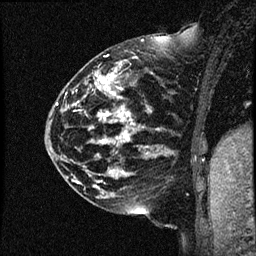
Breast MRI (dynamic contrast-enhanced), one sagittal slice; position 16 of 44 along the scan axis; dynamic contrast-enhanced study with each time point stored as its own series, time point 2 of 4 at this slice position (early post-contrast, ordered by acquisition time); 1.5 T; TE 4.2 ms, TR 17.7 ms; 2 mm slice thickness; 256 × 256 image matrix, field of view 200 × 200 mm. Female patient, age 52 years. From the clinical record (not read from this slice): setting: breast cancer imaged before/during neoadjuvant chemotherapy; receptor status: HR-positive, HER2-negative.
Outlined on this slice (semi-automatically segmented with operator editing):
- analysis volume of interest (the breast-tissue region the enhancement analysis was run in; not a lesion): bounding box (x1, y1, x2, y2) in pixels: (47, 48, 163, 147)
- tumour enhancement mask (voxels above the 100 % enhancement threshold inside the analysis volume of interest): (85, 68, 159, 143)